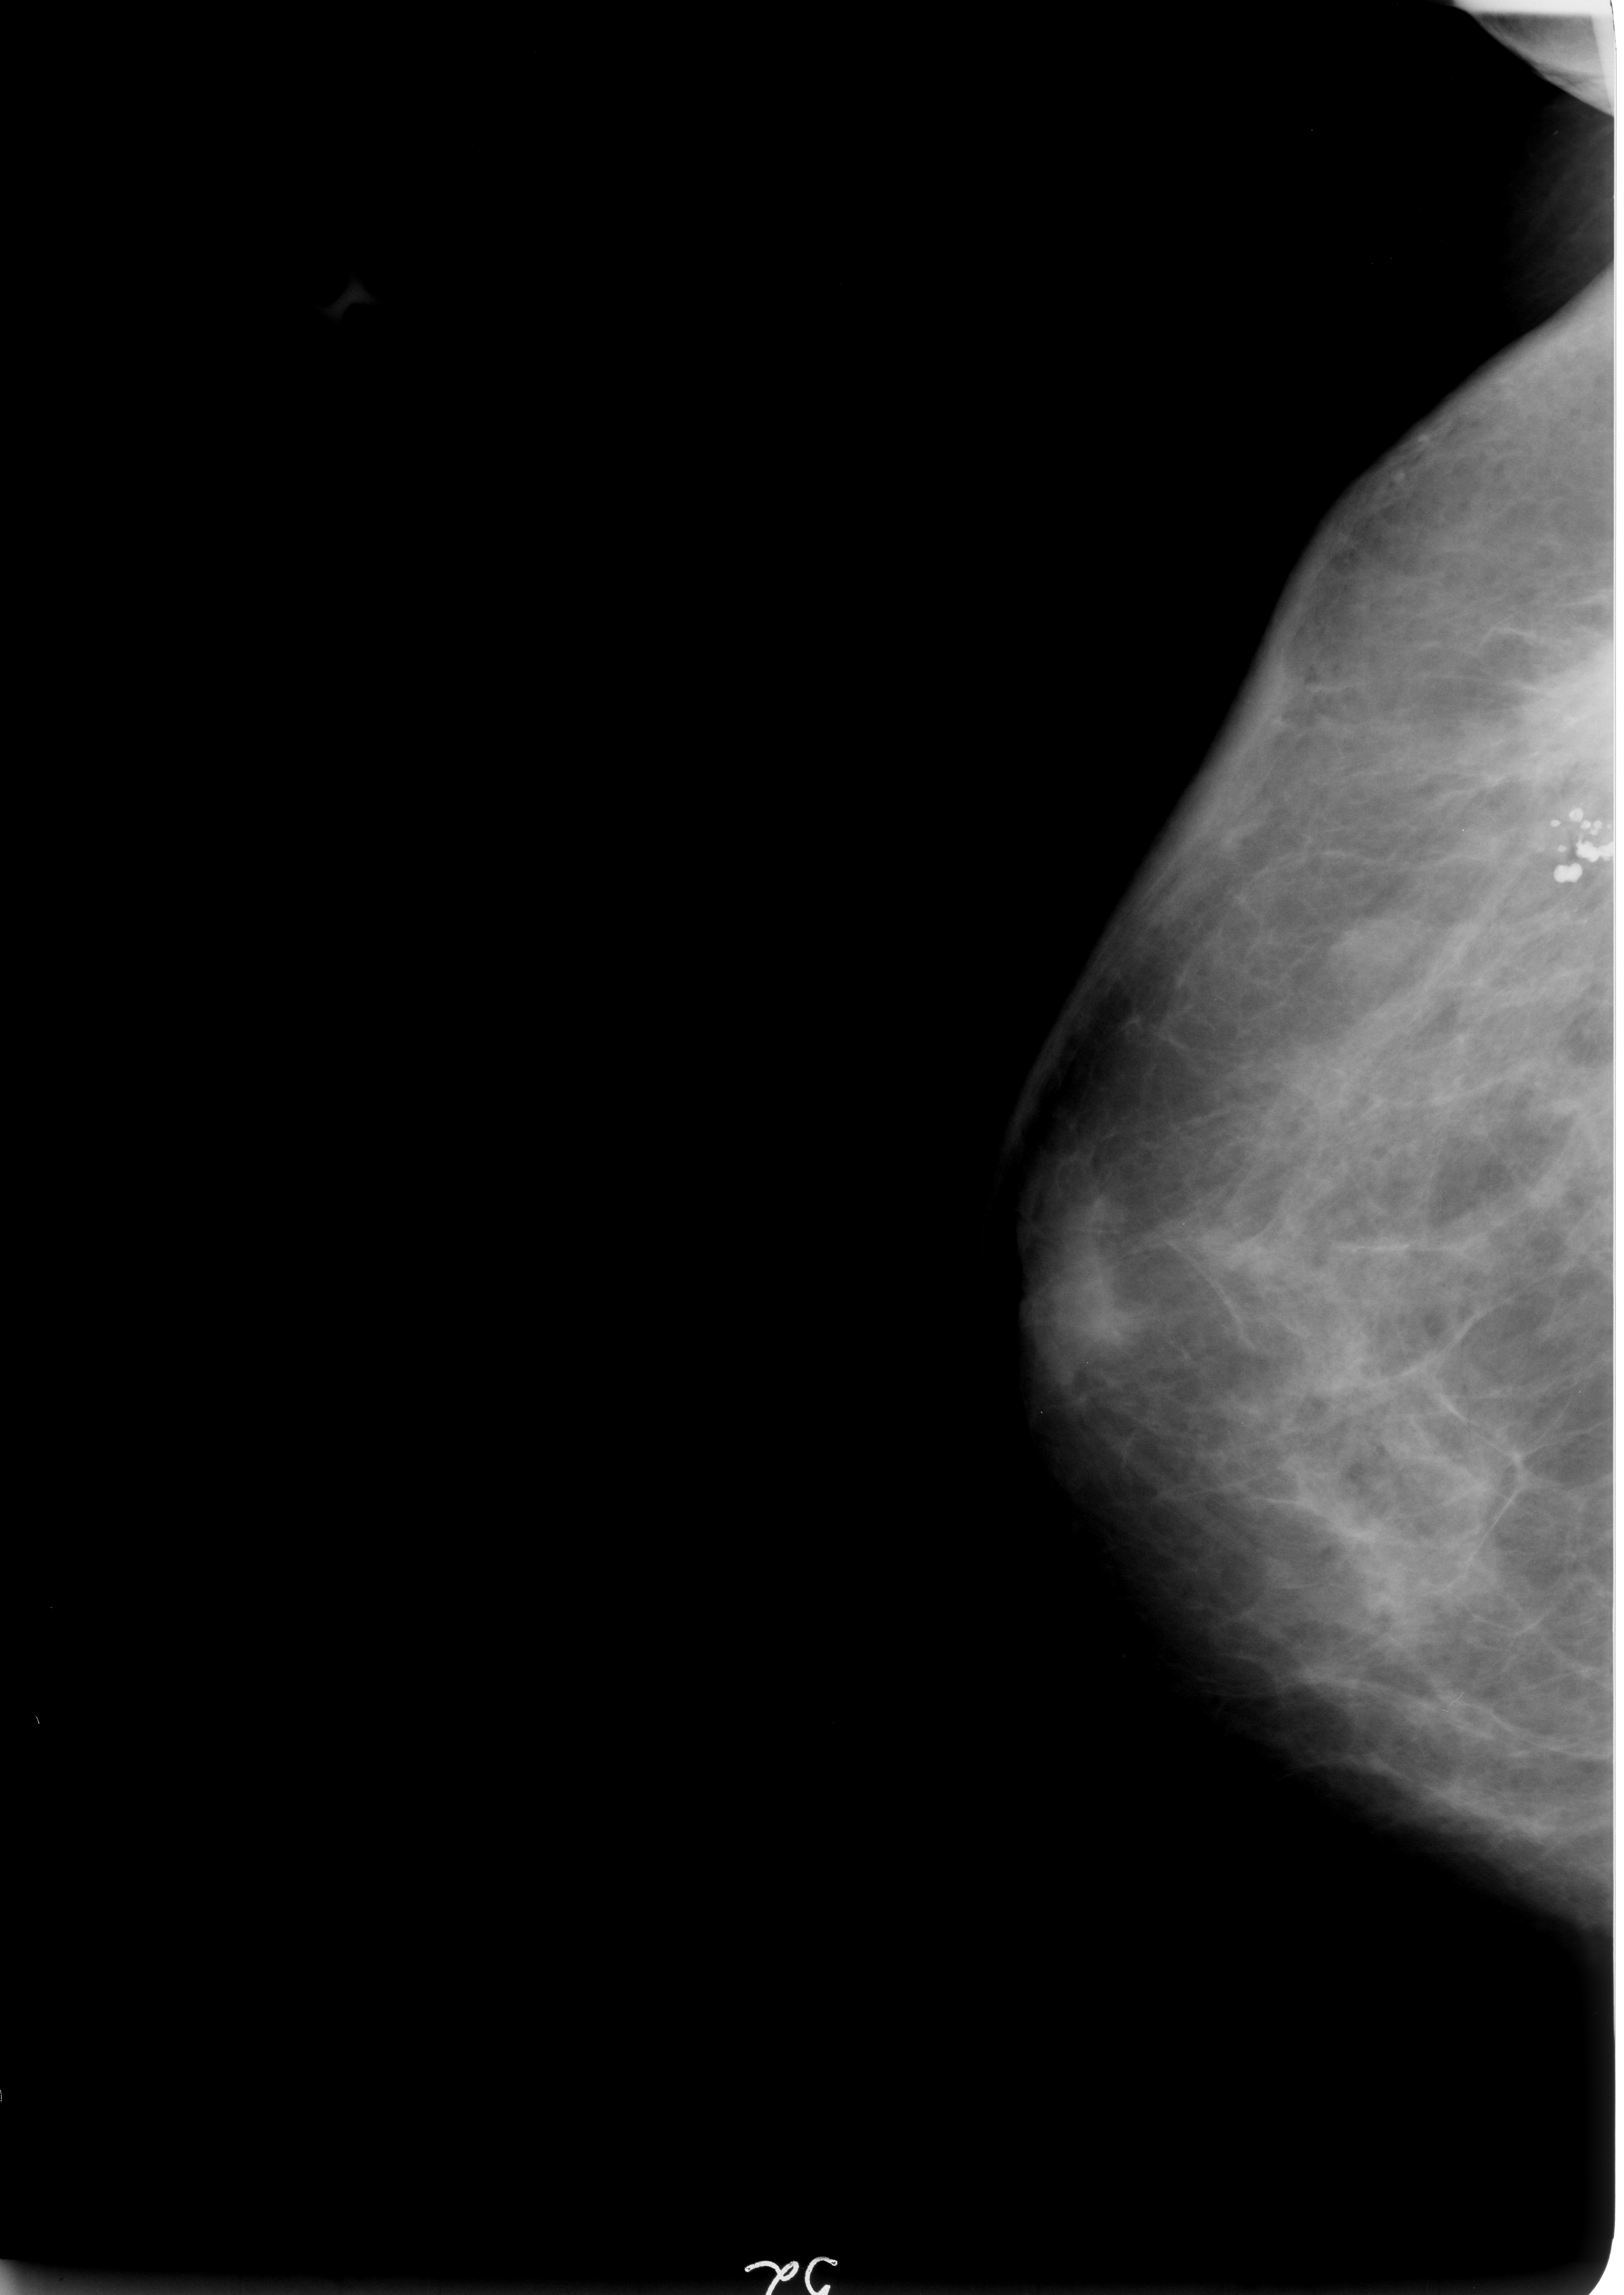
Scanned film-screen mammogram. Right breast. Craniocaudal (CC) view. BI-RADS breast density category 2 (scale 1–4). 1624 × 2295 image matrix.
Expert-marked regions of interest on this image (one box per marked abnormality):
- Finding 1 of 2: calcifications, morphology pleomorphic / fine linear branching, distribution segmental; BI-RADS assessment category 5; subtlety rating 5 on a 1 (subtle) to 5 (obvious) scale; pathology (as recorded): malignant: bounding box (x1, y1, x2, y2) in pixels: (1550, 848, 1580, 894)
- Finding 2 of 2: calcifications, morphology pleomorphic / fine linear branching, distribution segmental; BI-RADS assessment category 5; subtlety rating 5 on a 1 (subtle) to 5 (obvious) scale; pathology result (as recorded, not read from the image): malignant: (1573, 832, 1612, 862)